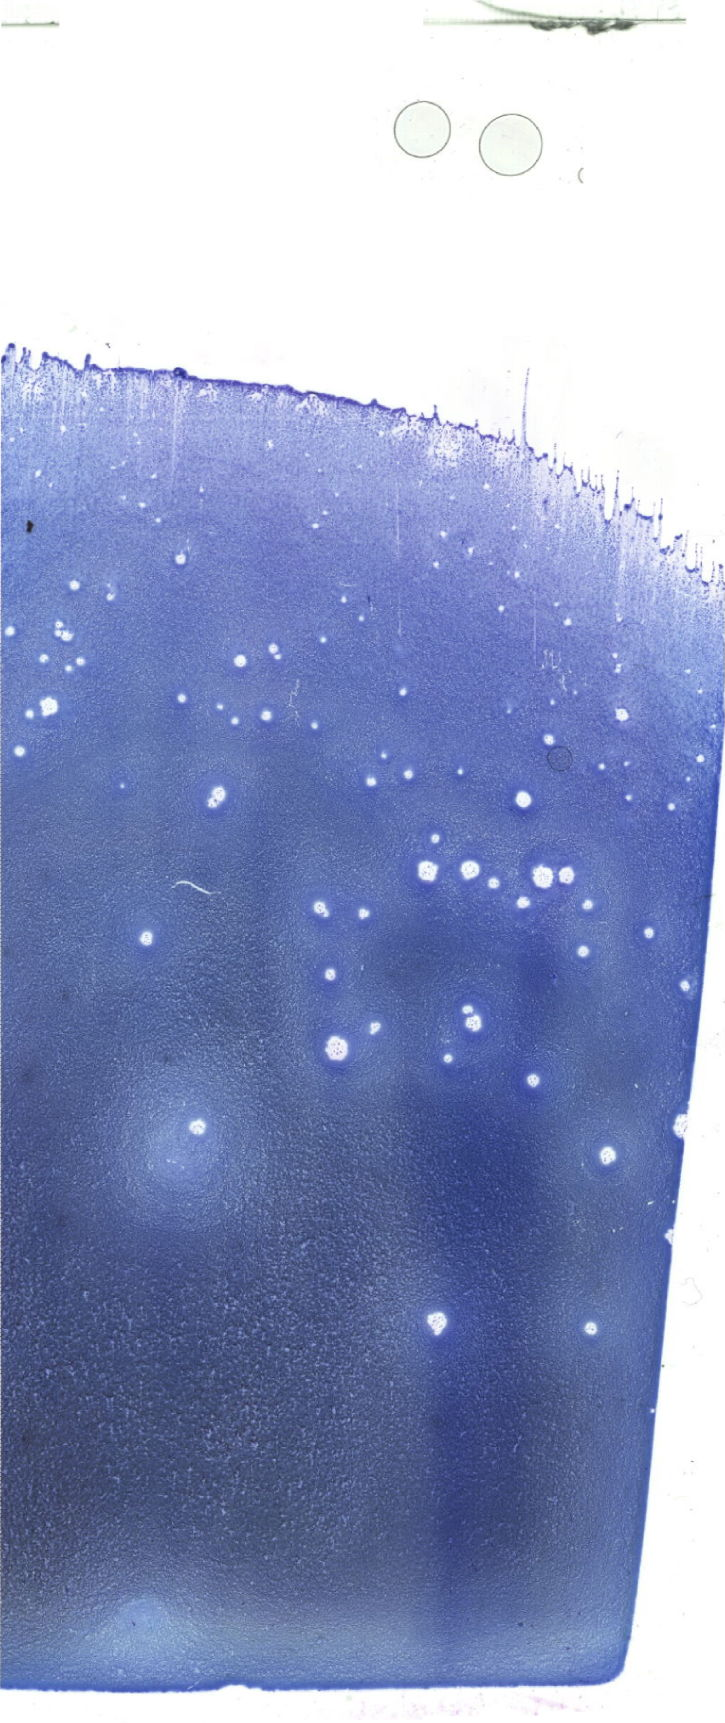
Bone marrow aspirate smear, May-Grünwald–Giemsa stain, whole-slide image — shown as a low-resolution overview of the whole scanned area (about 20.6 x 48.8 mm). Male patient.
Diagnosis: Acute Promyelocytic Leukemia with t(15;17)(q24.1;q21.2);PML-RARA.